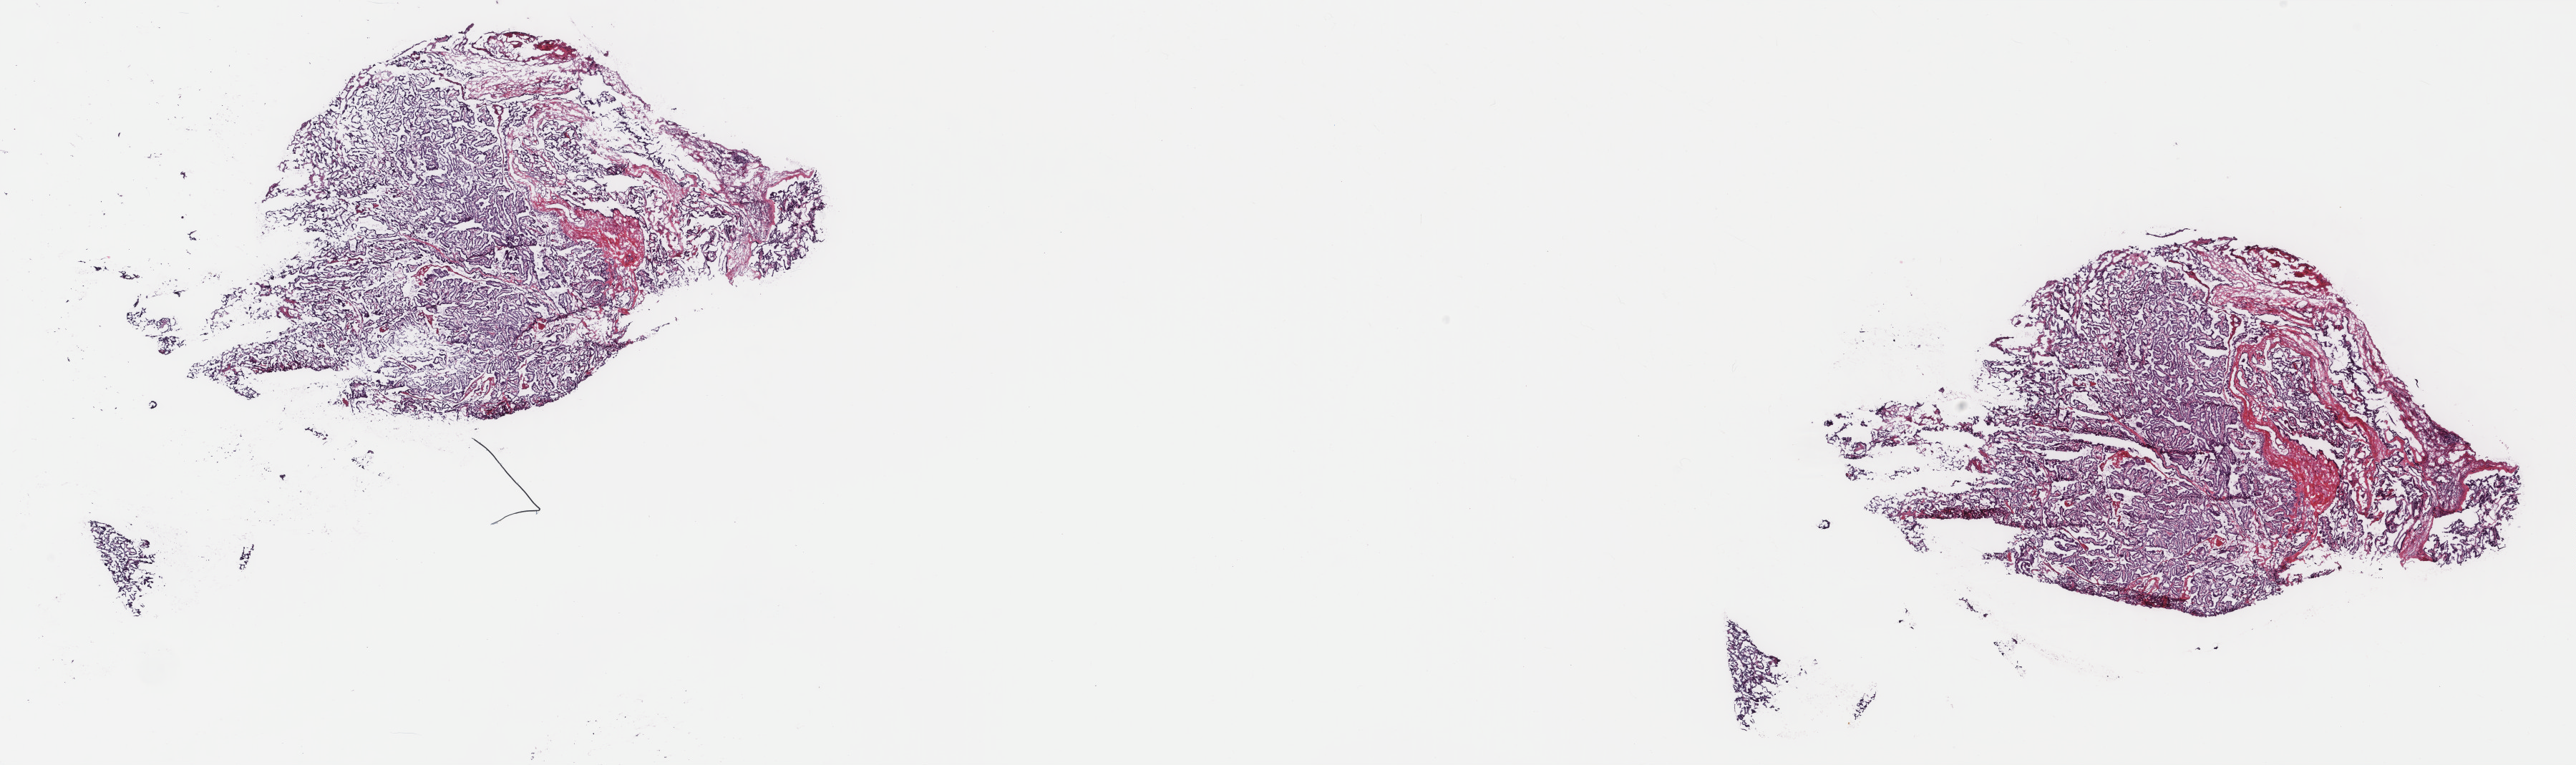
Hematoxylin and eosin (H&E) stained whole-slide image — shown as a low-resolution overview of the whole scanned area (about 28.6 x 8.5 mm), frozen section from the top of the tissue portion, thyroid, primary tumour sample. Male, age 57 years at initial diagnosis. Composition of this section per pathologist review: tumour cells 98%, tumour nuclei 85%, normal cells 0%, stromal cells 2%, necrosis 0%. Infiltration values recorded for this section: lymphocyte infiltration 0%, monocyte infiltration 0%, neutrophil infiltration 0%.
AJCC pathologic stage: IVA (7th edition). Laterality: bilateral. Histologic diagnosis: Papillary adenocarcinoma, NOS (thyroid gland).